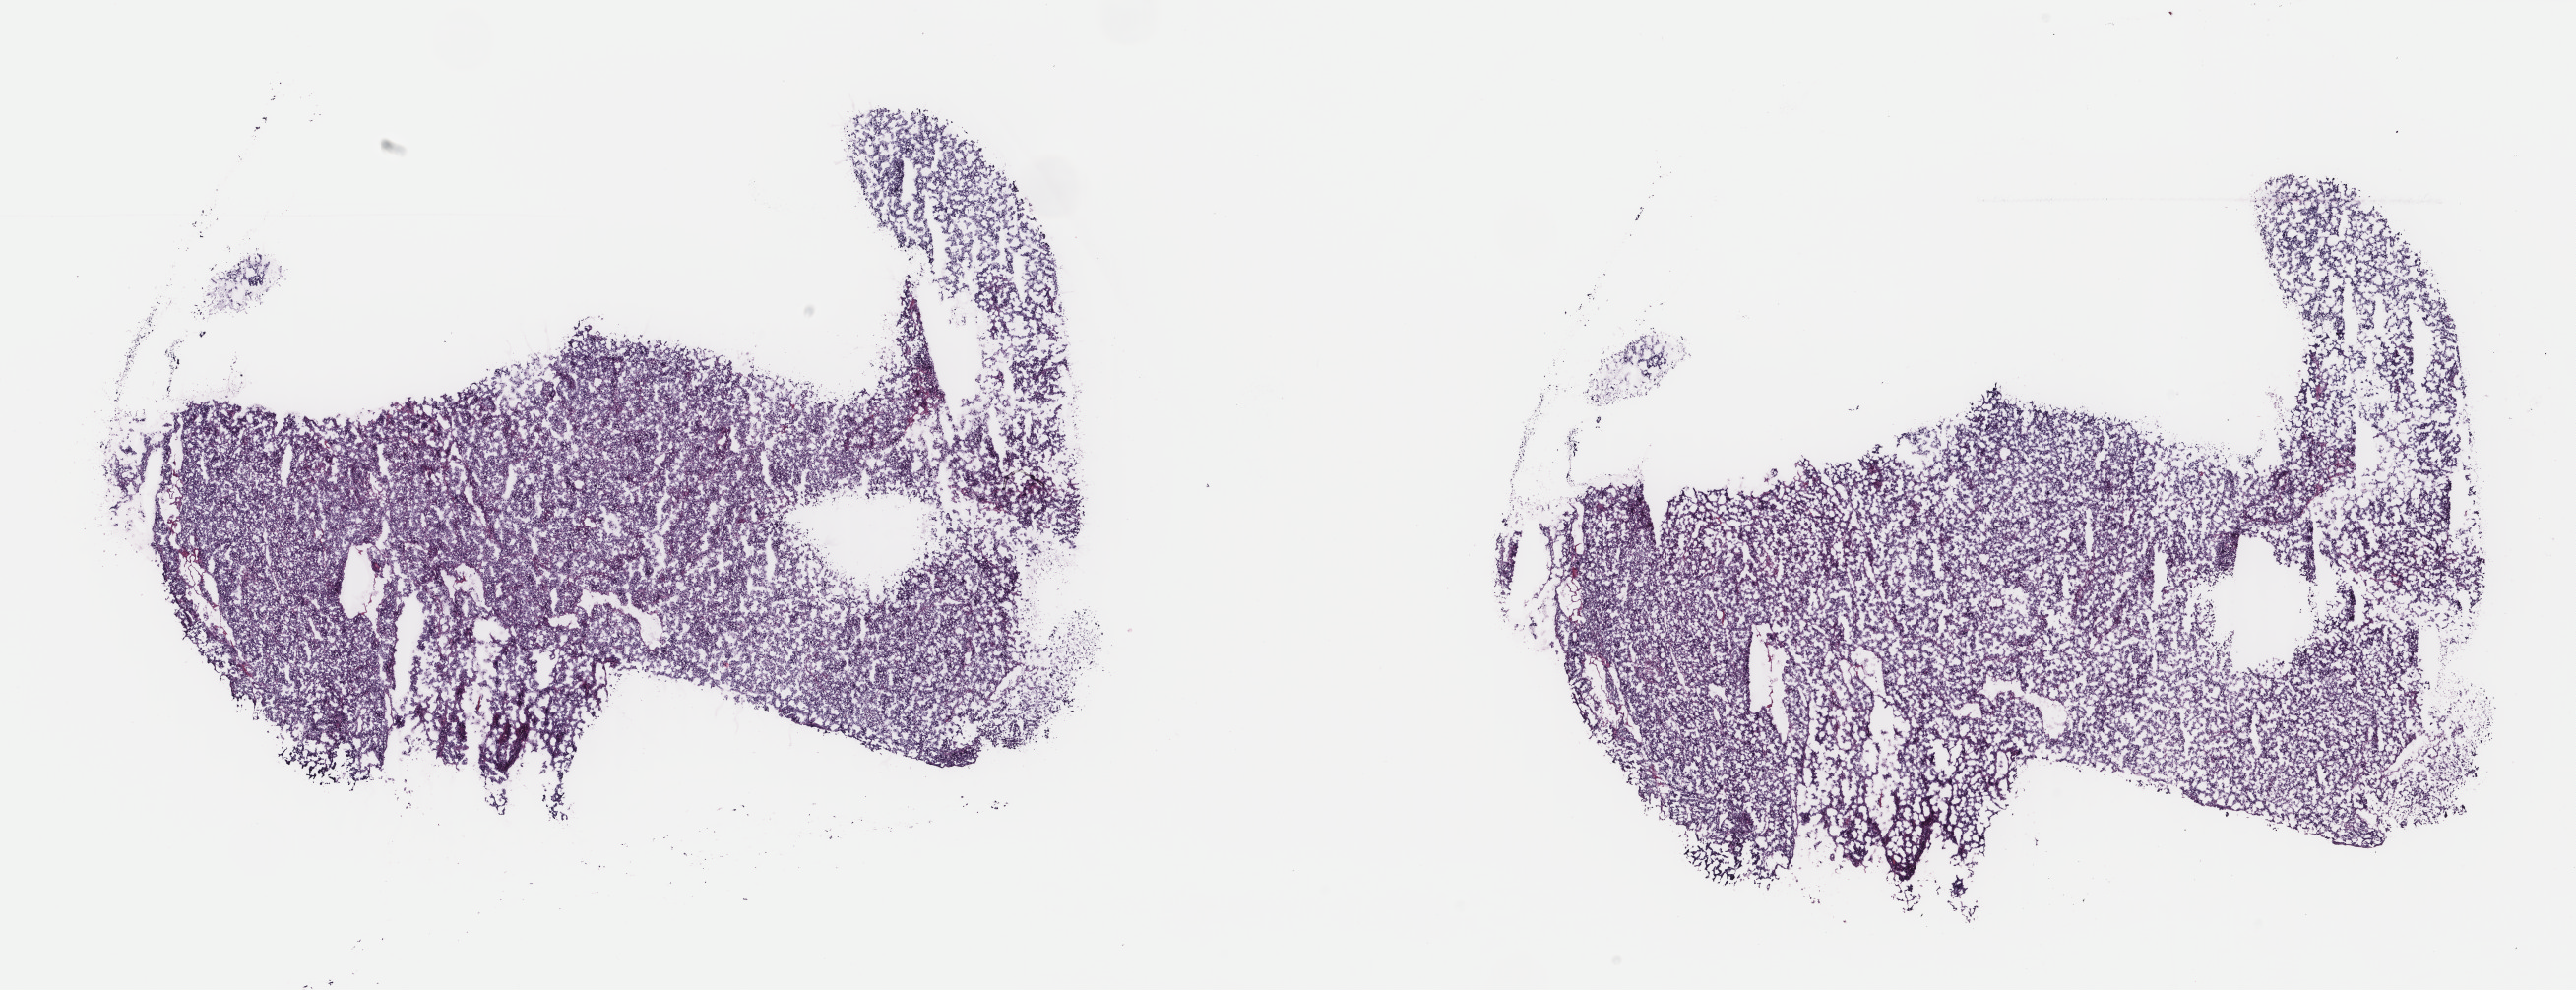
Whole-slide histology image, H&E, a low-resolution overview of the entire scanned area, about 20.8 x 8.0 mm, frozen section from the top of the tissue portion, uterus, primary tumour sample. Female patient; age at initial diagnosis 86 years. Histologic grade: G3 (poorly differentiated). Composition of this section per pathologist review: tumour cells 97%, tumour nuclei 96%, normal cells 0%, stromal cells 1%, necrosis 2%. Inflammatory infiltration, as recorded: lymphocyte infiltration 1%, monocyte infiltration 0%, neutrophil infiltration 0%.
FIGO stage: IIA. Pathologic diagnosis: Serous cystadenocarcinoma, NOS (endometrium).